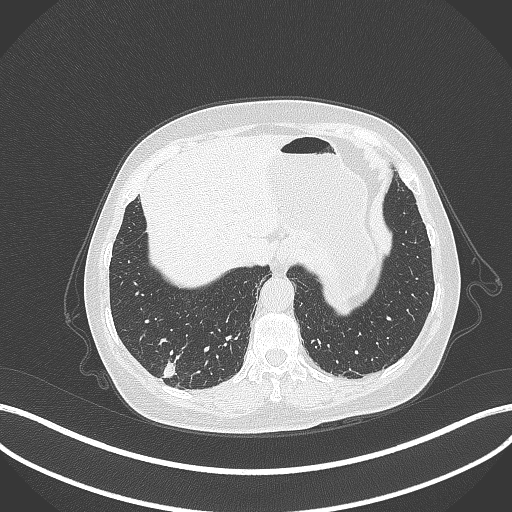
Chest CT, one axial slice. Slice 48 of 333 in the series (ordered by position). Reconstruction kernel B70f. 120 kVp. Lung window (W 1500 / L -600 HU). 1 mm slice thickness. 512 × 512 image matrix. Female patient, age 69 years. From the clinical record (not read from this slice): clinical TNM (as recorded): T1b N0 M0; histopathological grade: G2-3.
Structures marked on this image (bounding box drawn by a radiologist):
- lung tumour (recorded histology: adenocarcinoma): box from (x=158, y=354) to (x=179, y=381) px